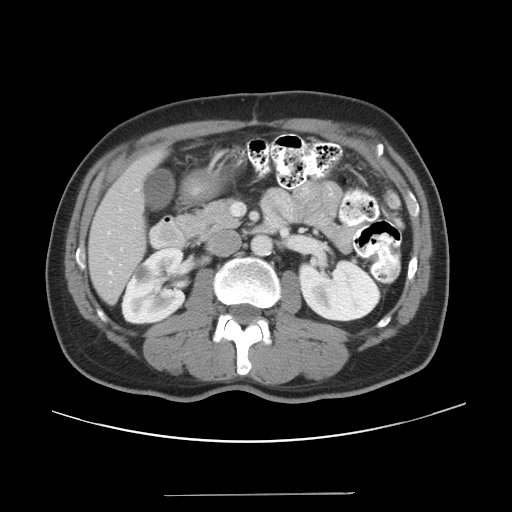
Contrast-enhanced abdominal CT, one axial slice; slice 14 of 43 in the series (ordered by position); 120 kVp; intravenous contrast given; soft-tissue window (W 400 / L 40 HU); 5 mm slice thickness; 512 × 512 image matrix. Male patient, age 65 years. From the clinical record (not read from this slice): diagnosis: colorectal cancer liver metastases, imaged before liver resection; multiple liver metastases: no; largest metastasis: 3.8 cm; disease in both lobes: no.
Structures marked on this image (manually delineated by an expert):
- hepatic veins: bounding box [x1, y1, x2, y2] px = [108, 232, 122, 274]
- liver: [89, 155, 162, 302]
- planned liver remnant (the part of the liver to remain after resection): [89, 155, 163, 302]